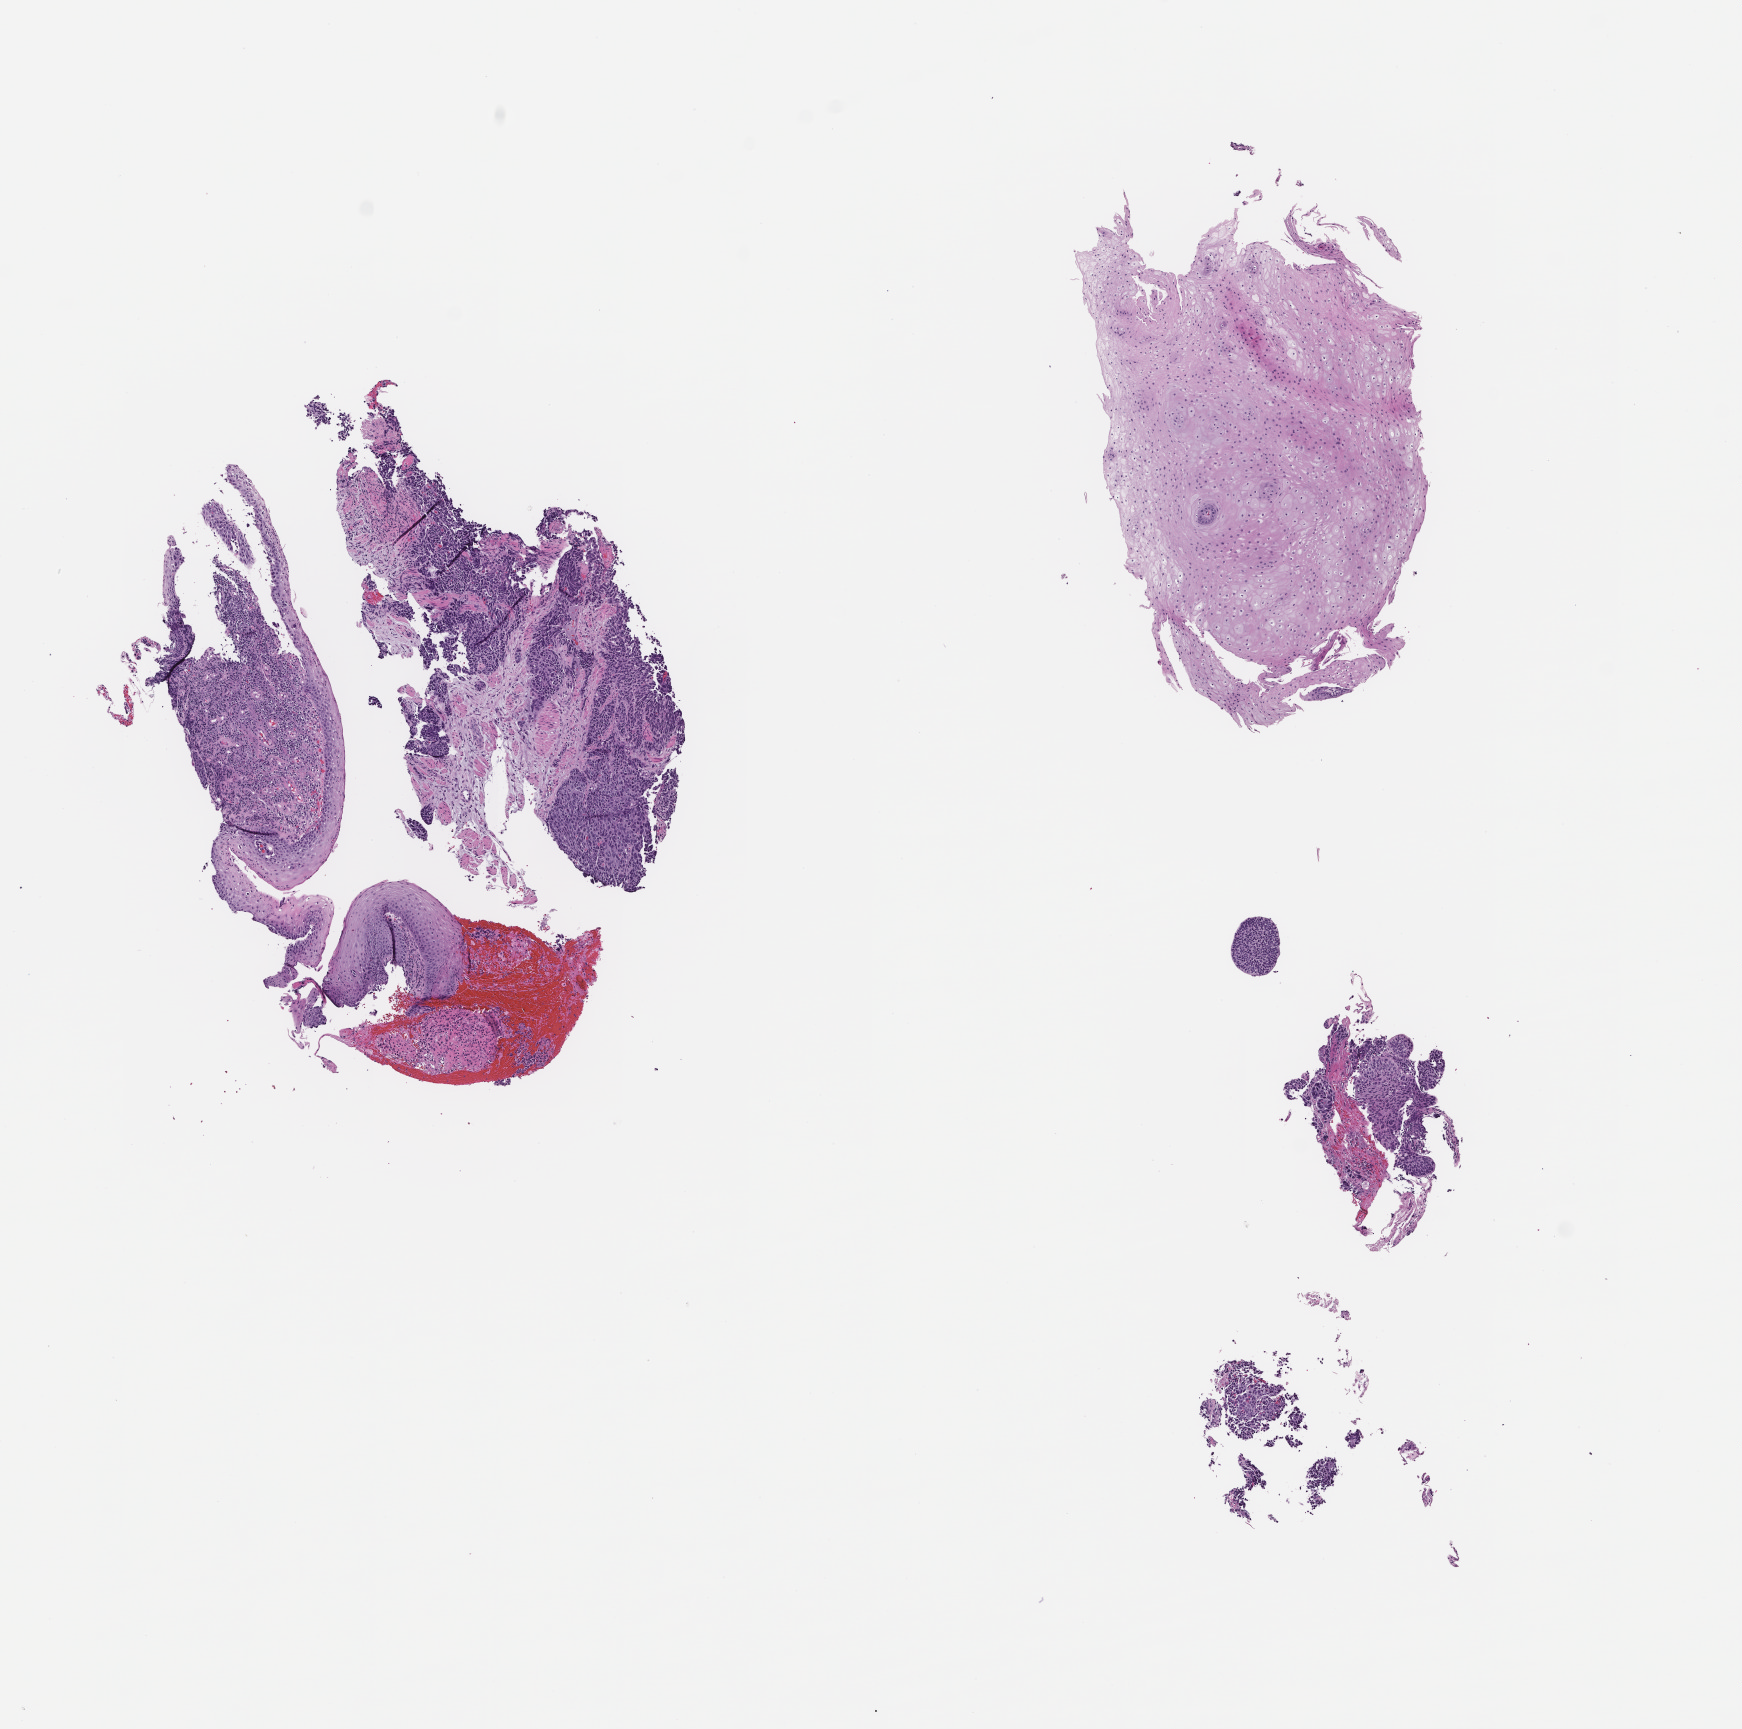
Whole-slide image, haematoxylin and eosin stain — a low-resolution overview of the entire scanned area, about 7.0 x 7.0 mm. Formalin-fixed paraffin-embedded section. Tissue site: esophagus. Patient sex: female.
This section: primary tumor. Diagnosis: Esophageal Carcinoma.